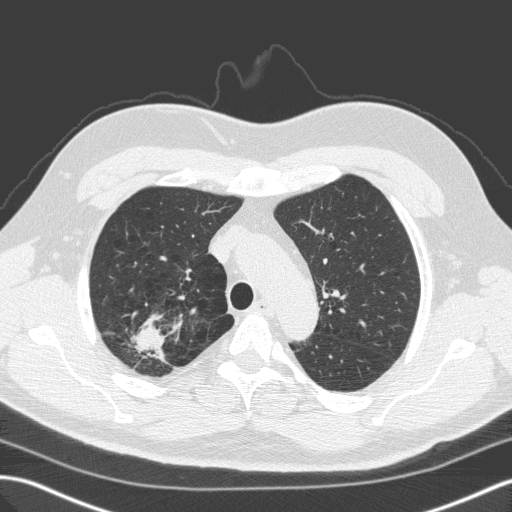
Low-dose screening chest CT, one axial slice; position 117 of 149 along the scan axis; 120 kVp; lung window (W 1500 / L -600 HU); 2 mm slice thickness; 512 × 512 image matrix, field of view 357 × 357 mm.
Outlined on this slice (manually delineated by an expert):
- lesion 1 (tumor, upper lobe of right lung): box from (x=134, y=324) to (x=165, y=353) px